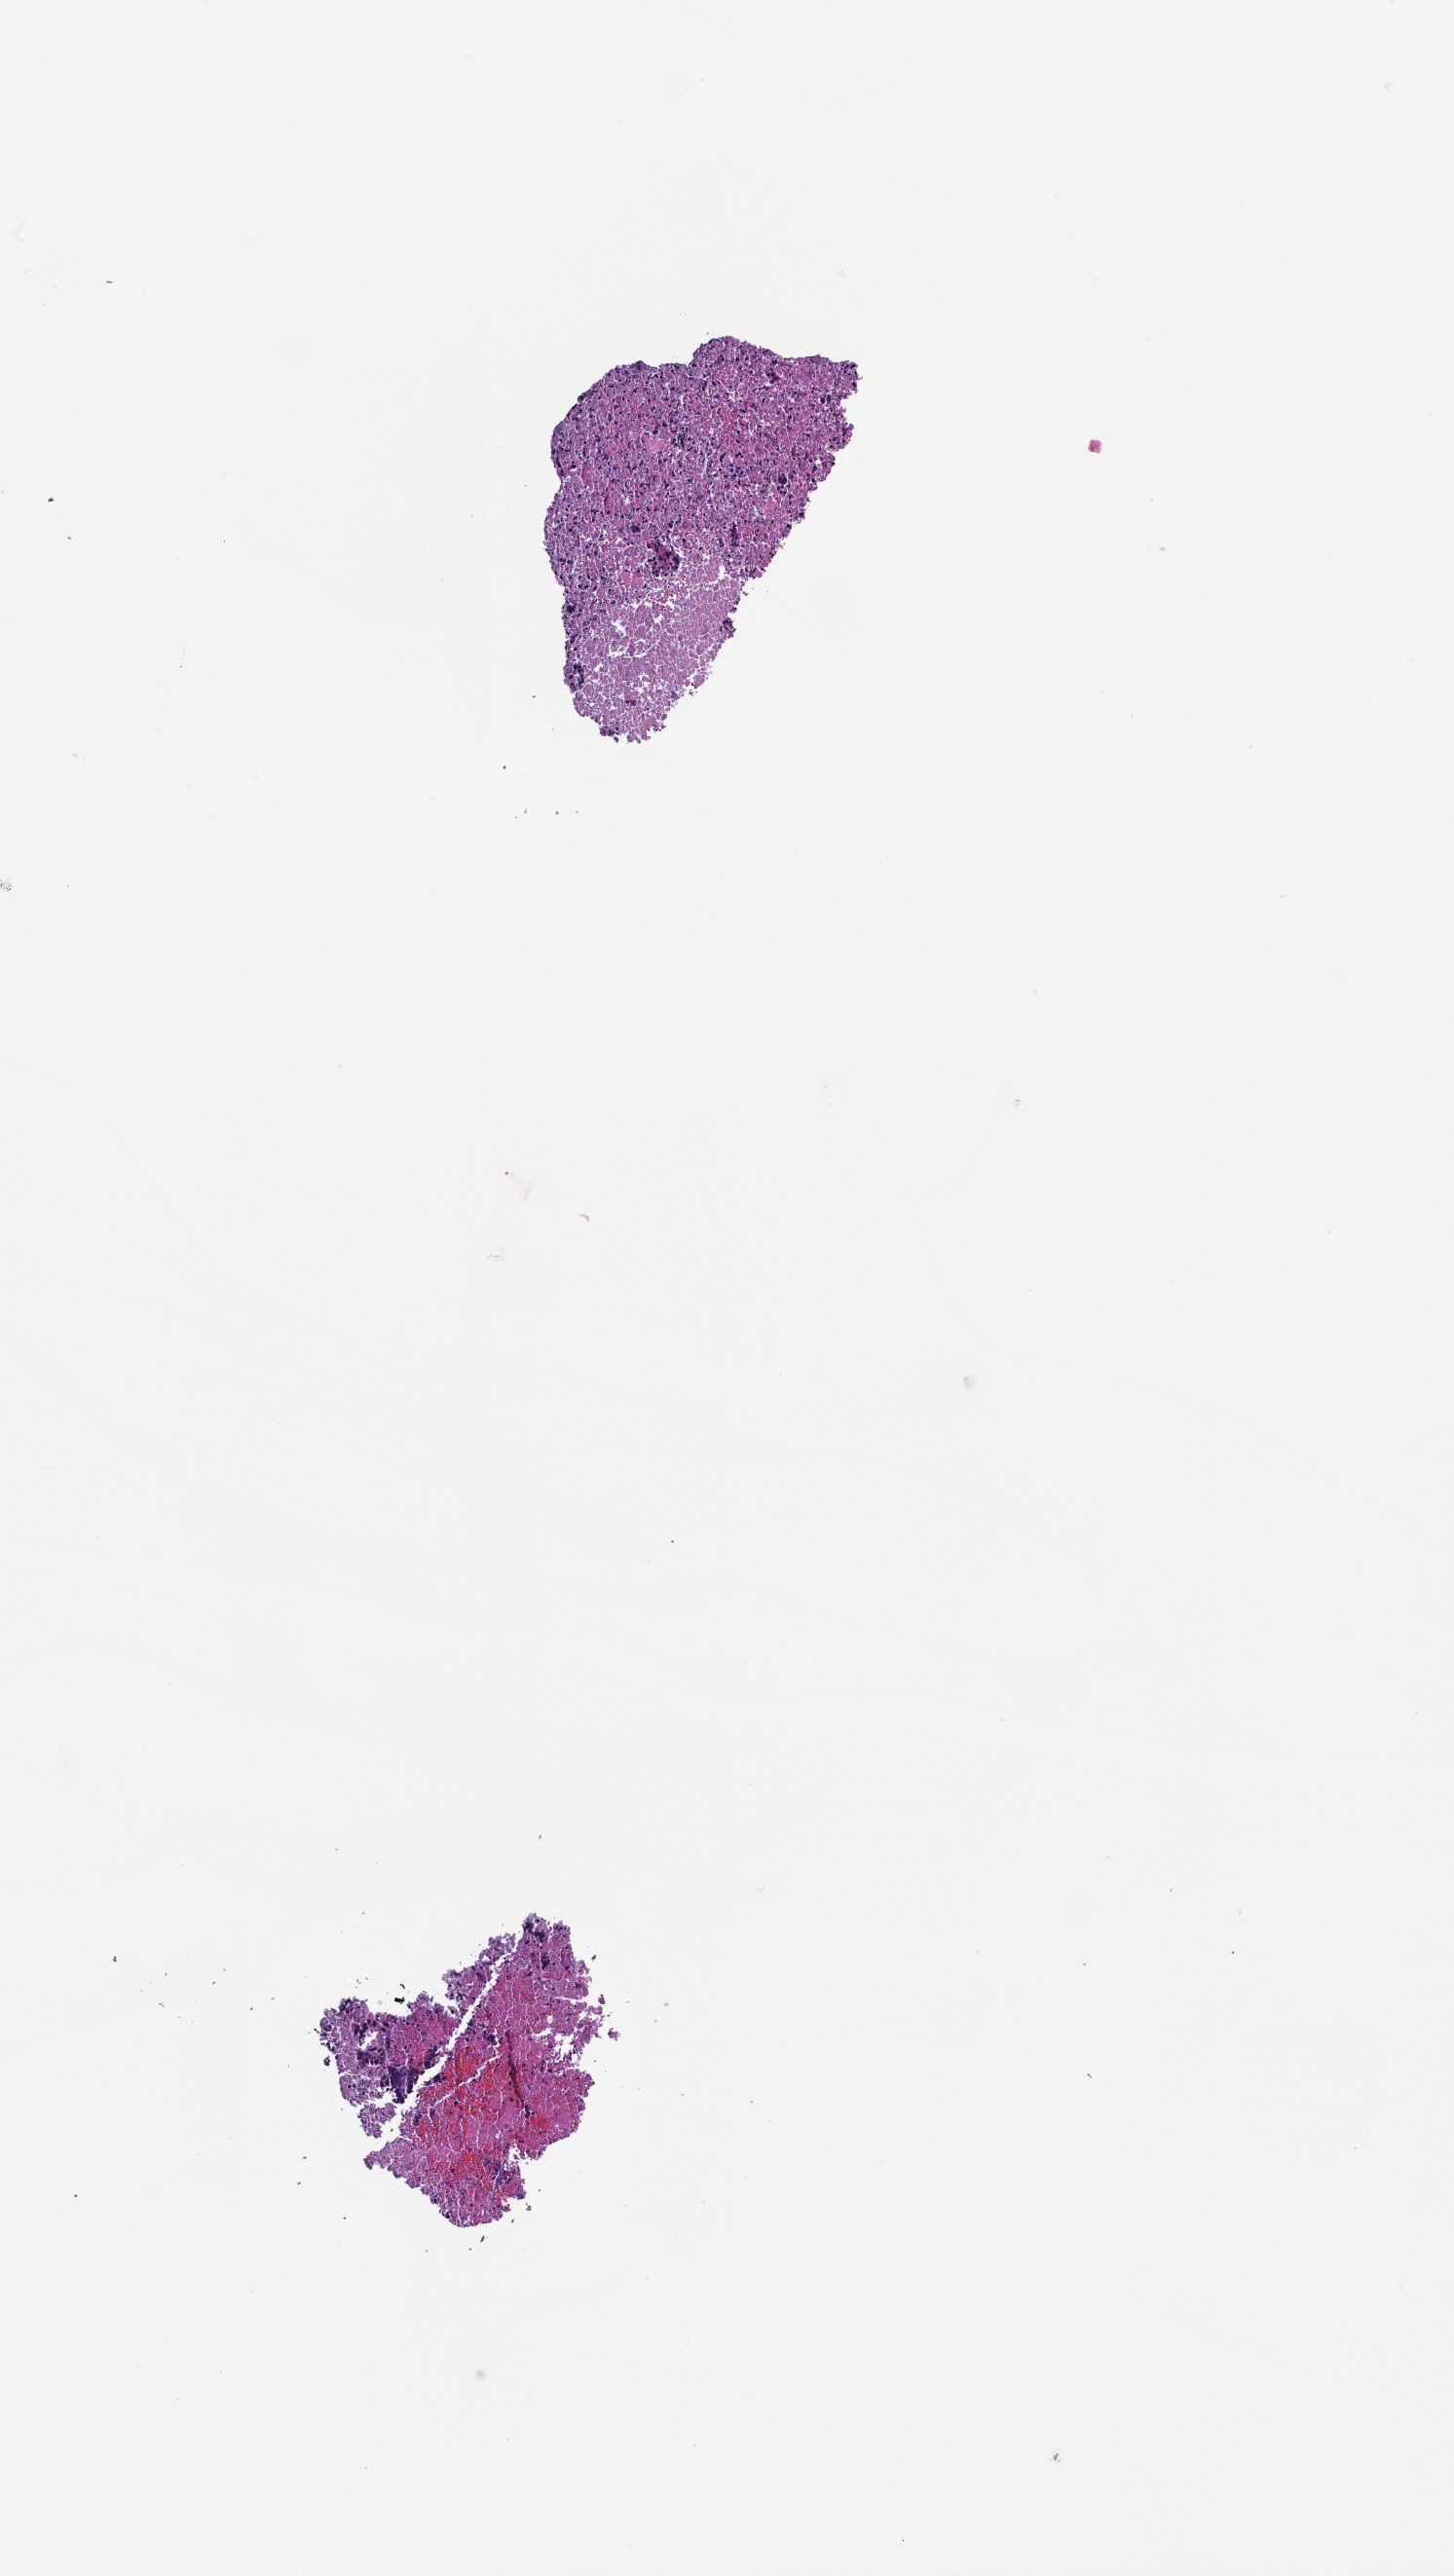
Digitized H&E-stained section — a low-resolution overview of the entire scanned area, about 3.0 x 5.3 mm, formalin-fixed, paraffin-embedded (FFPE) tissue, specimen time point: archival tissue. Male patient.
This section: metastatic tumor tissue. Patient diagnosis (primary): Colorectal Carcinoma.